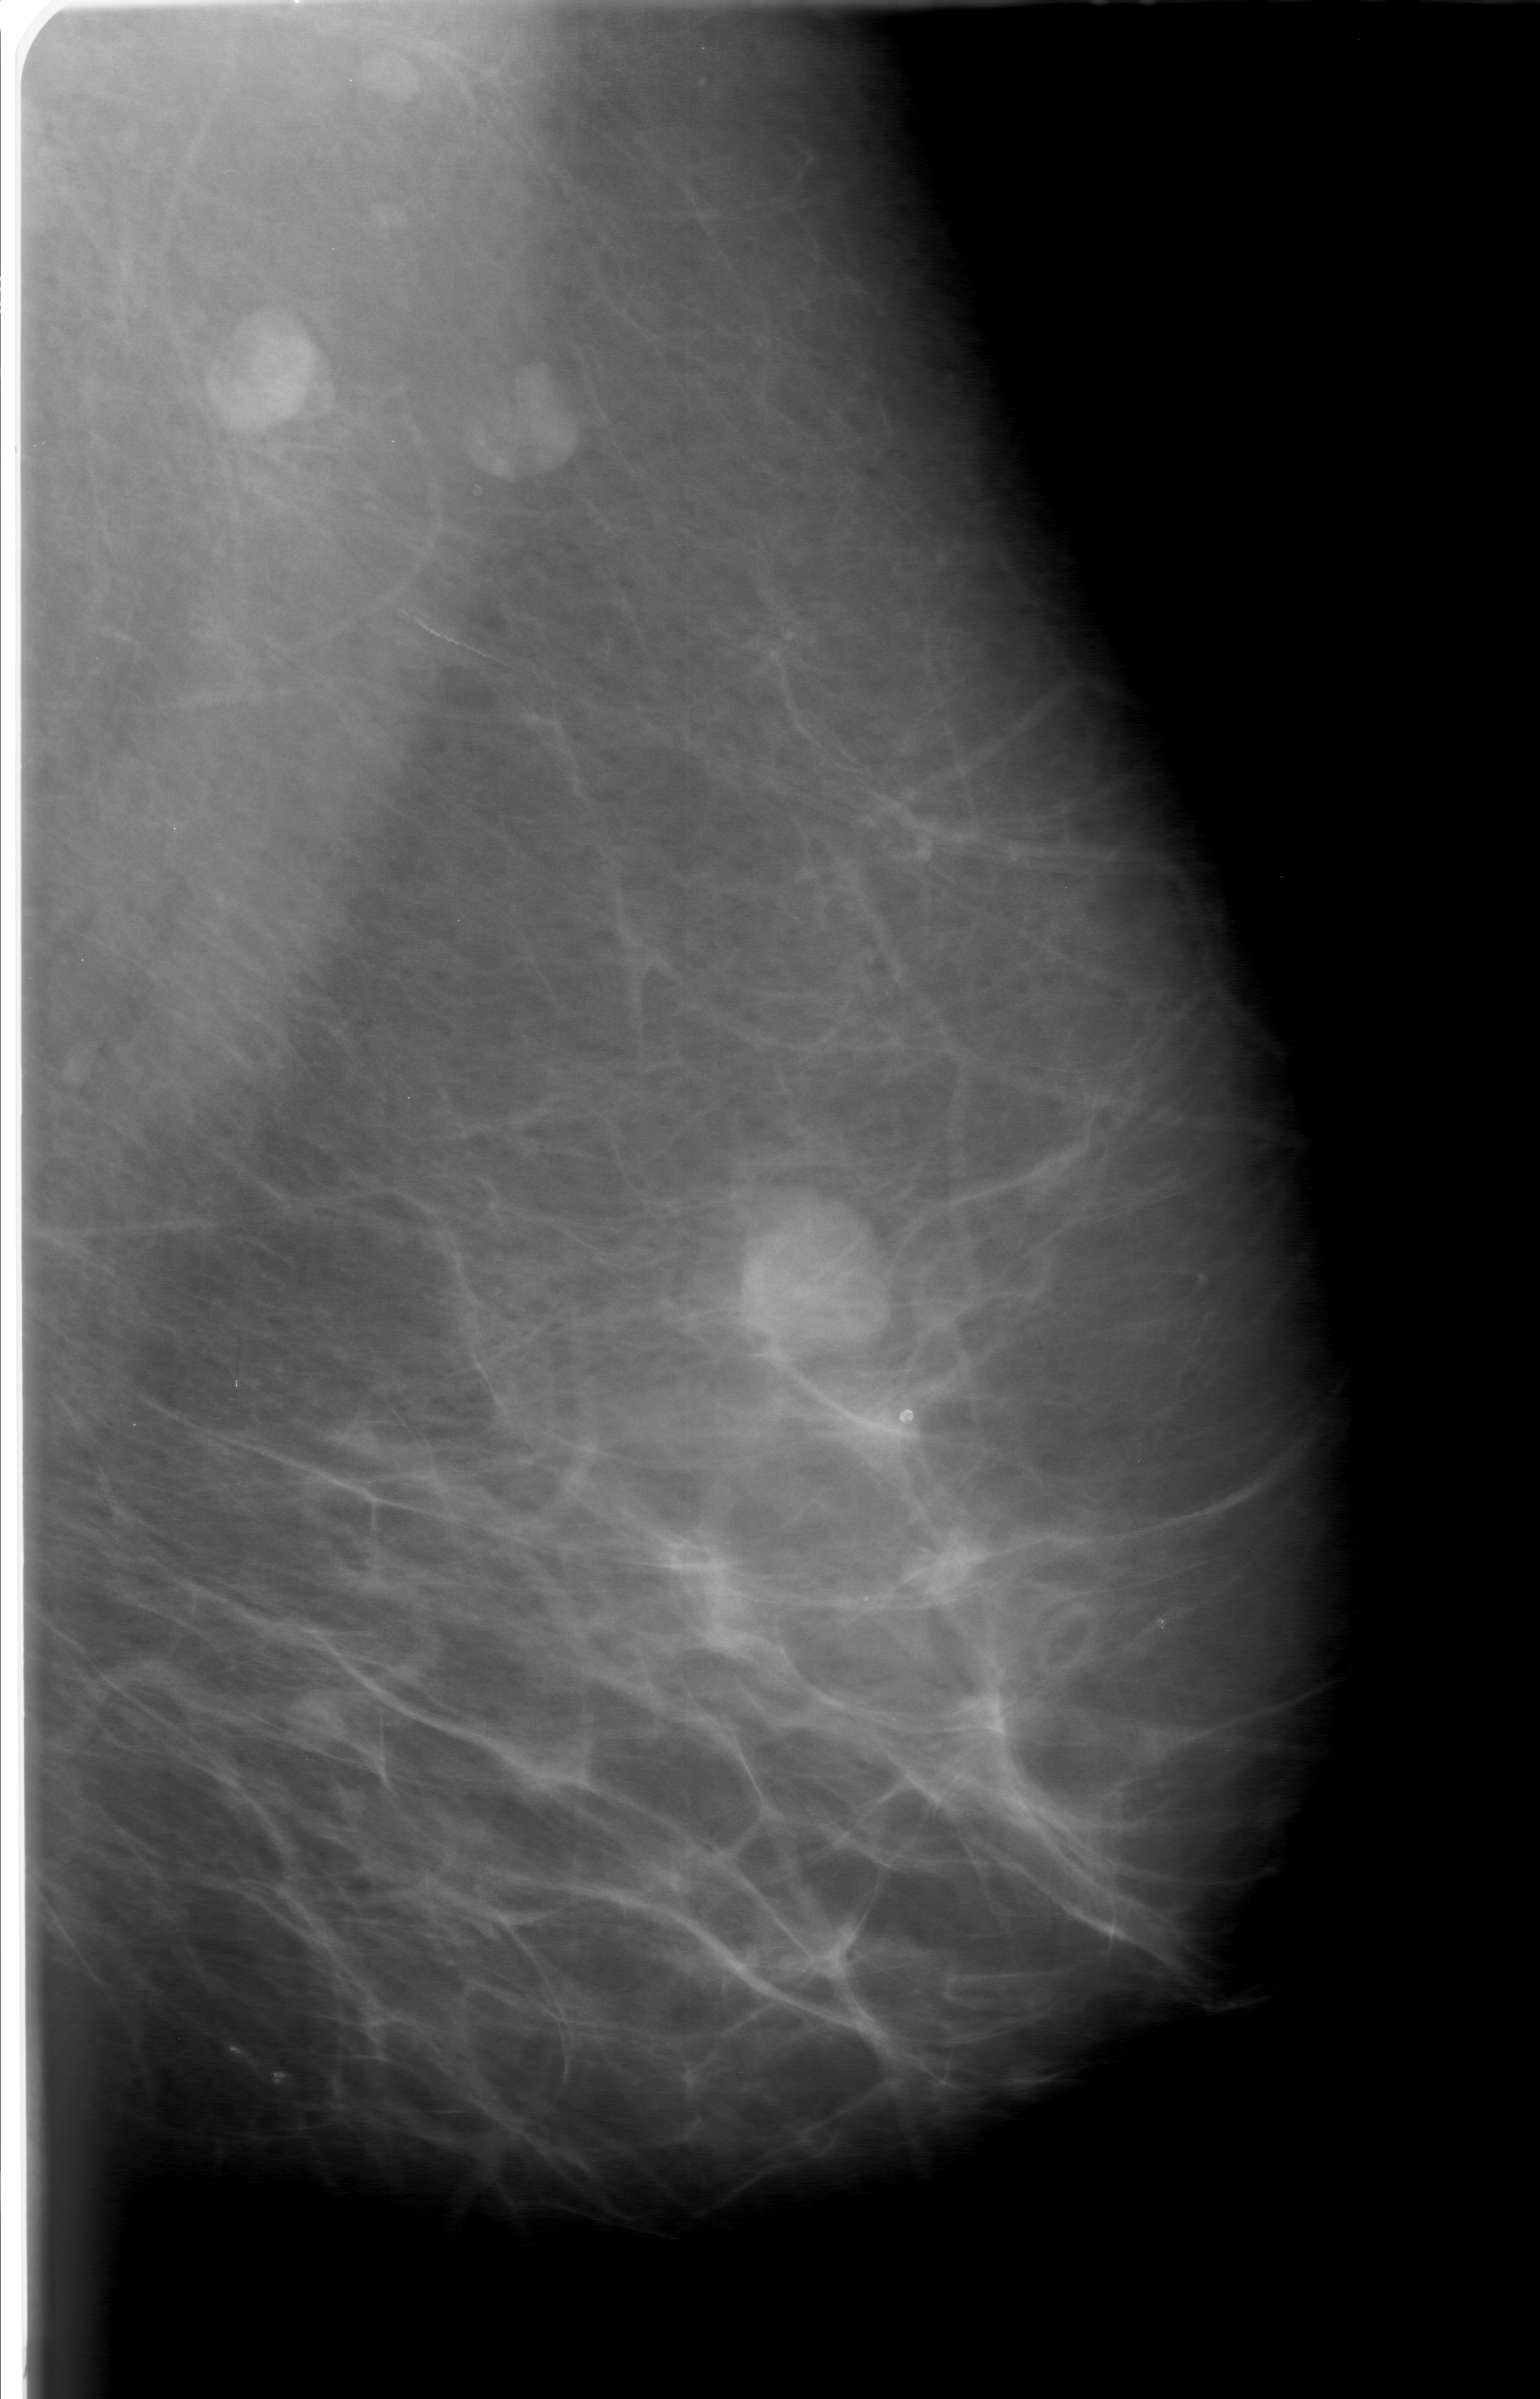
Mammogram (digitized film); left breast; MLO view; 1540 × 2399 image matrix.
Expert-marked regions of interest on this film, with their recorded descriptors:
- mass, shape lobulated, margins circumscribed; BI-RADS assessment category 0 (incomplete: needs additional imaging); subtlety rating 5 on a 1 (subtle) to 5 (obvious) scale; pathology result (as recorded, not read from the image): benign: box from (x=719, y=1184) to (x=899, y=1354) px